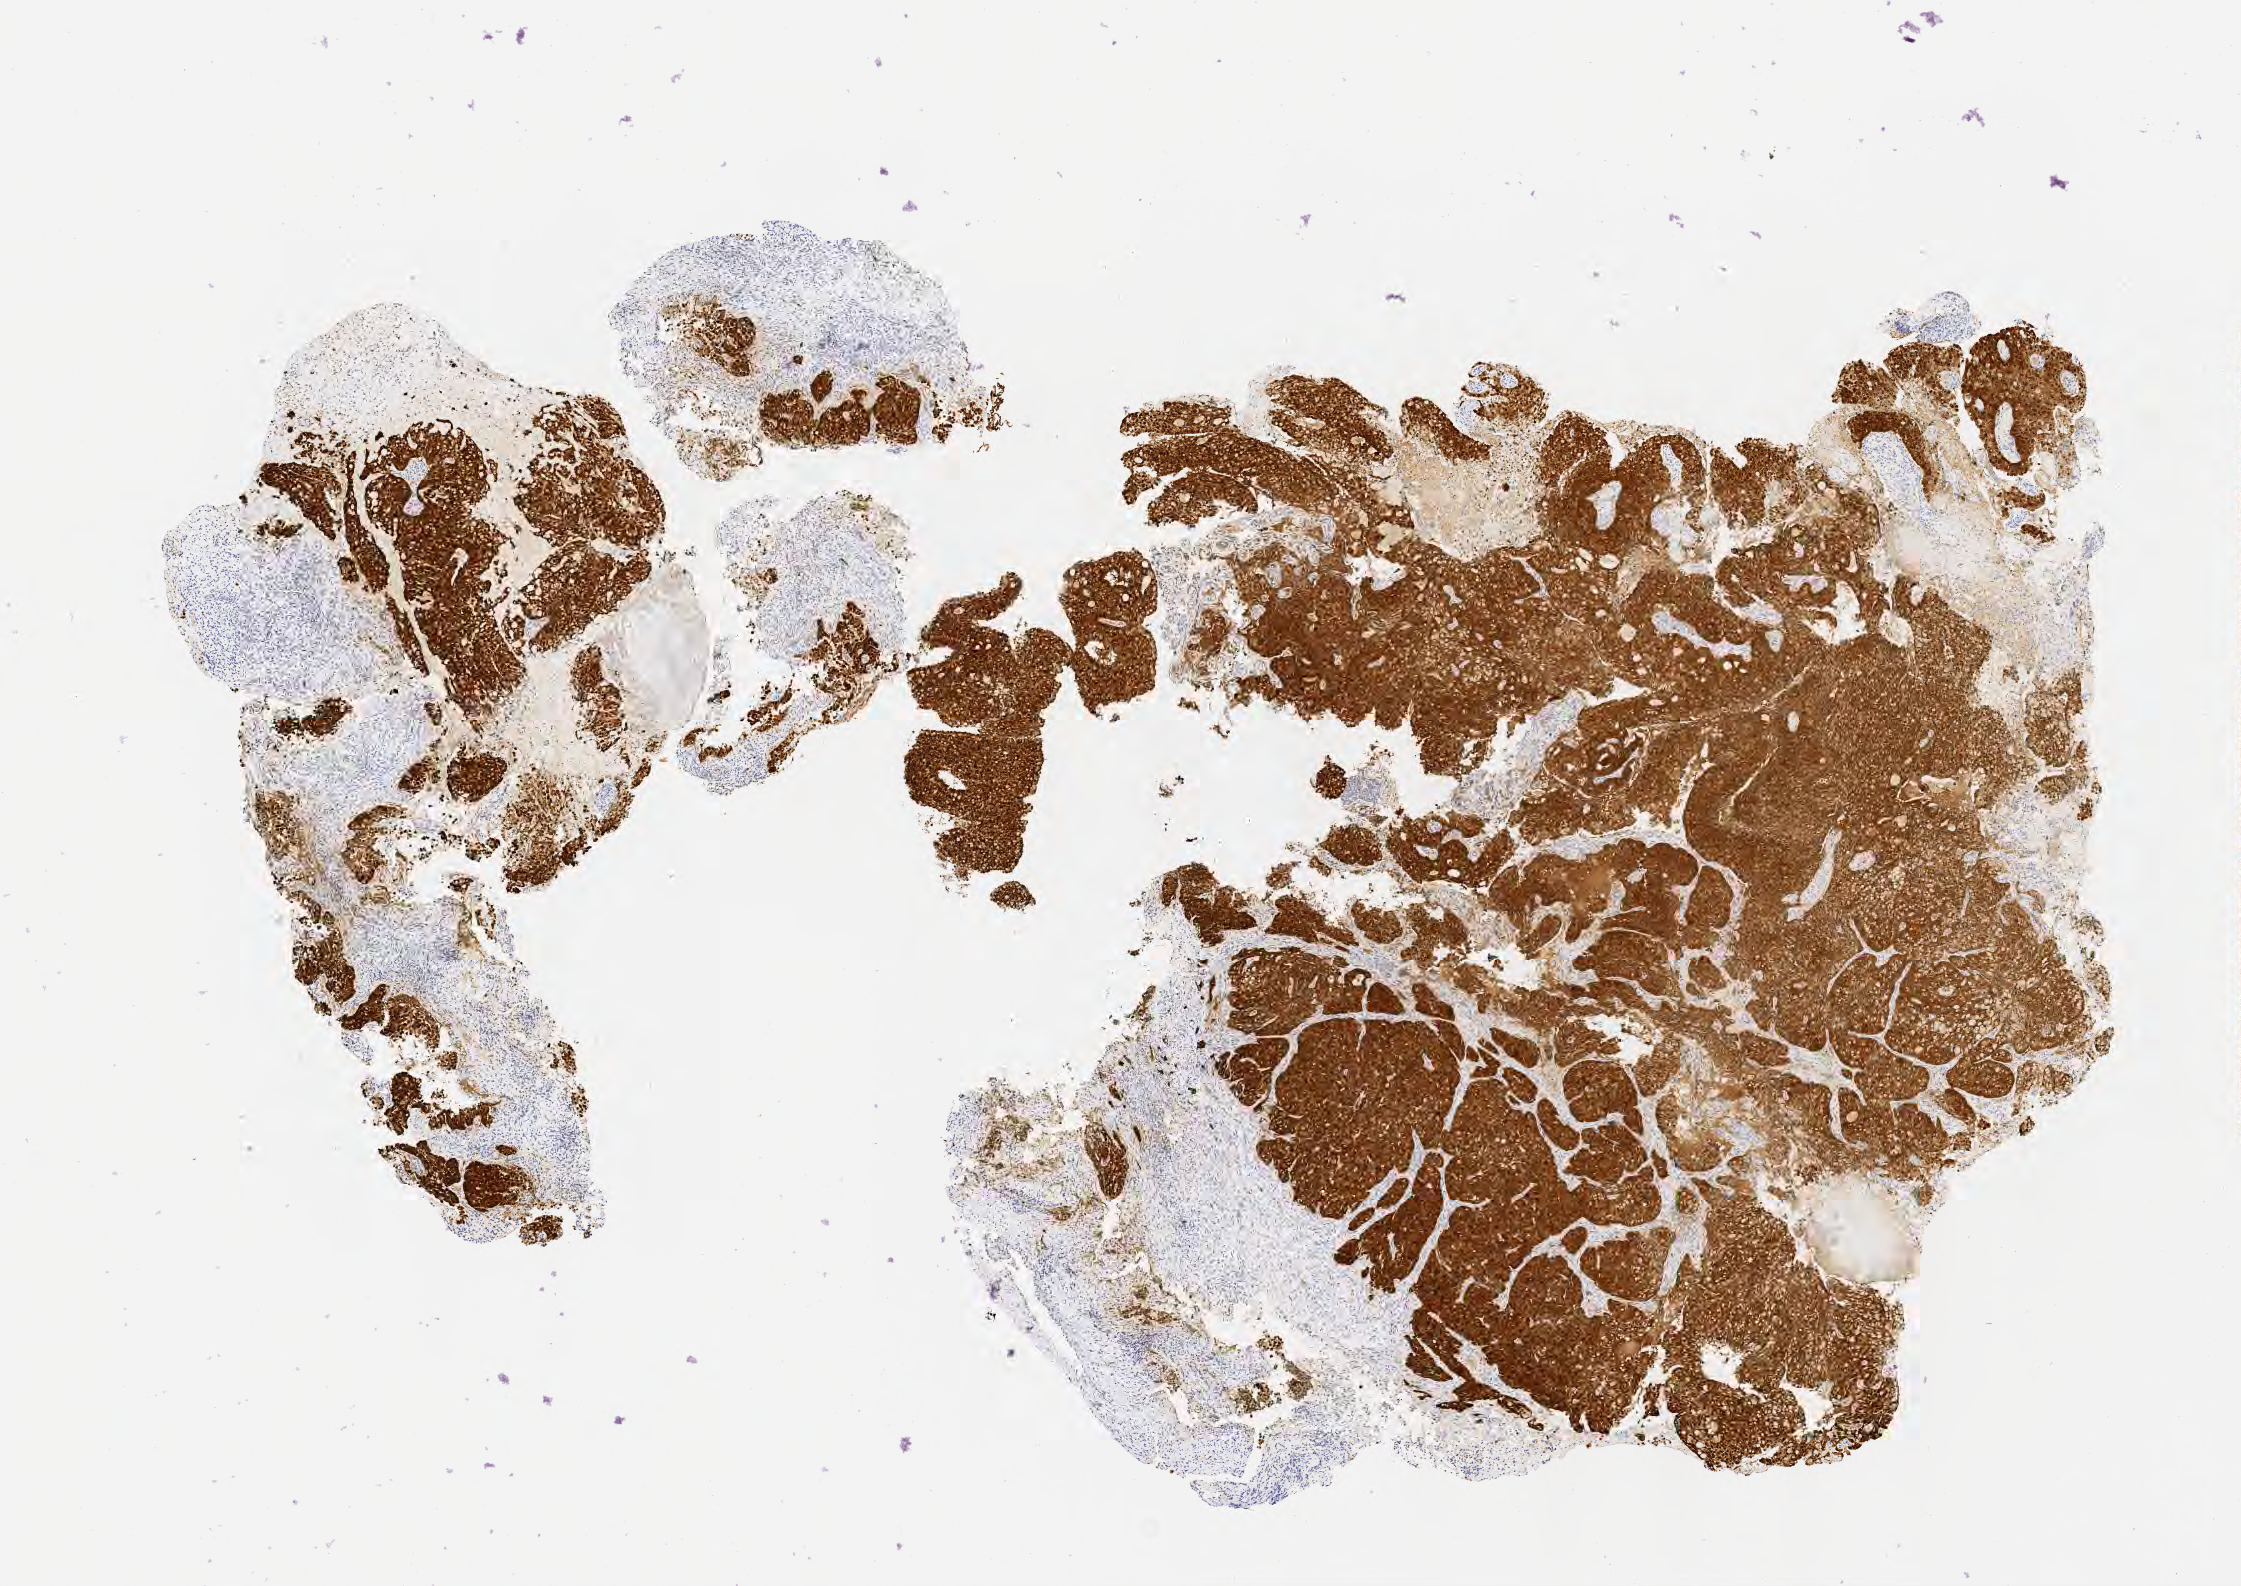
Immunohistochemistry (IHC) whole-slide image stained for p16 (p16INK4a) — shown as a low-resolution overview of the whole scanned area (about 9.1 x 6.4 mm). Tumor tissue. Anatomic site: cervix. Patient female; 40 years old.
- histologic diagnosis: Adenocarcinoma, NOS